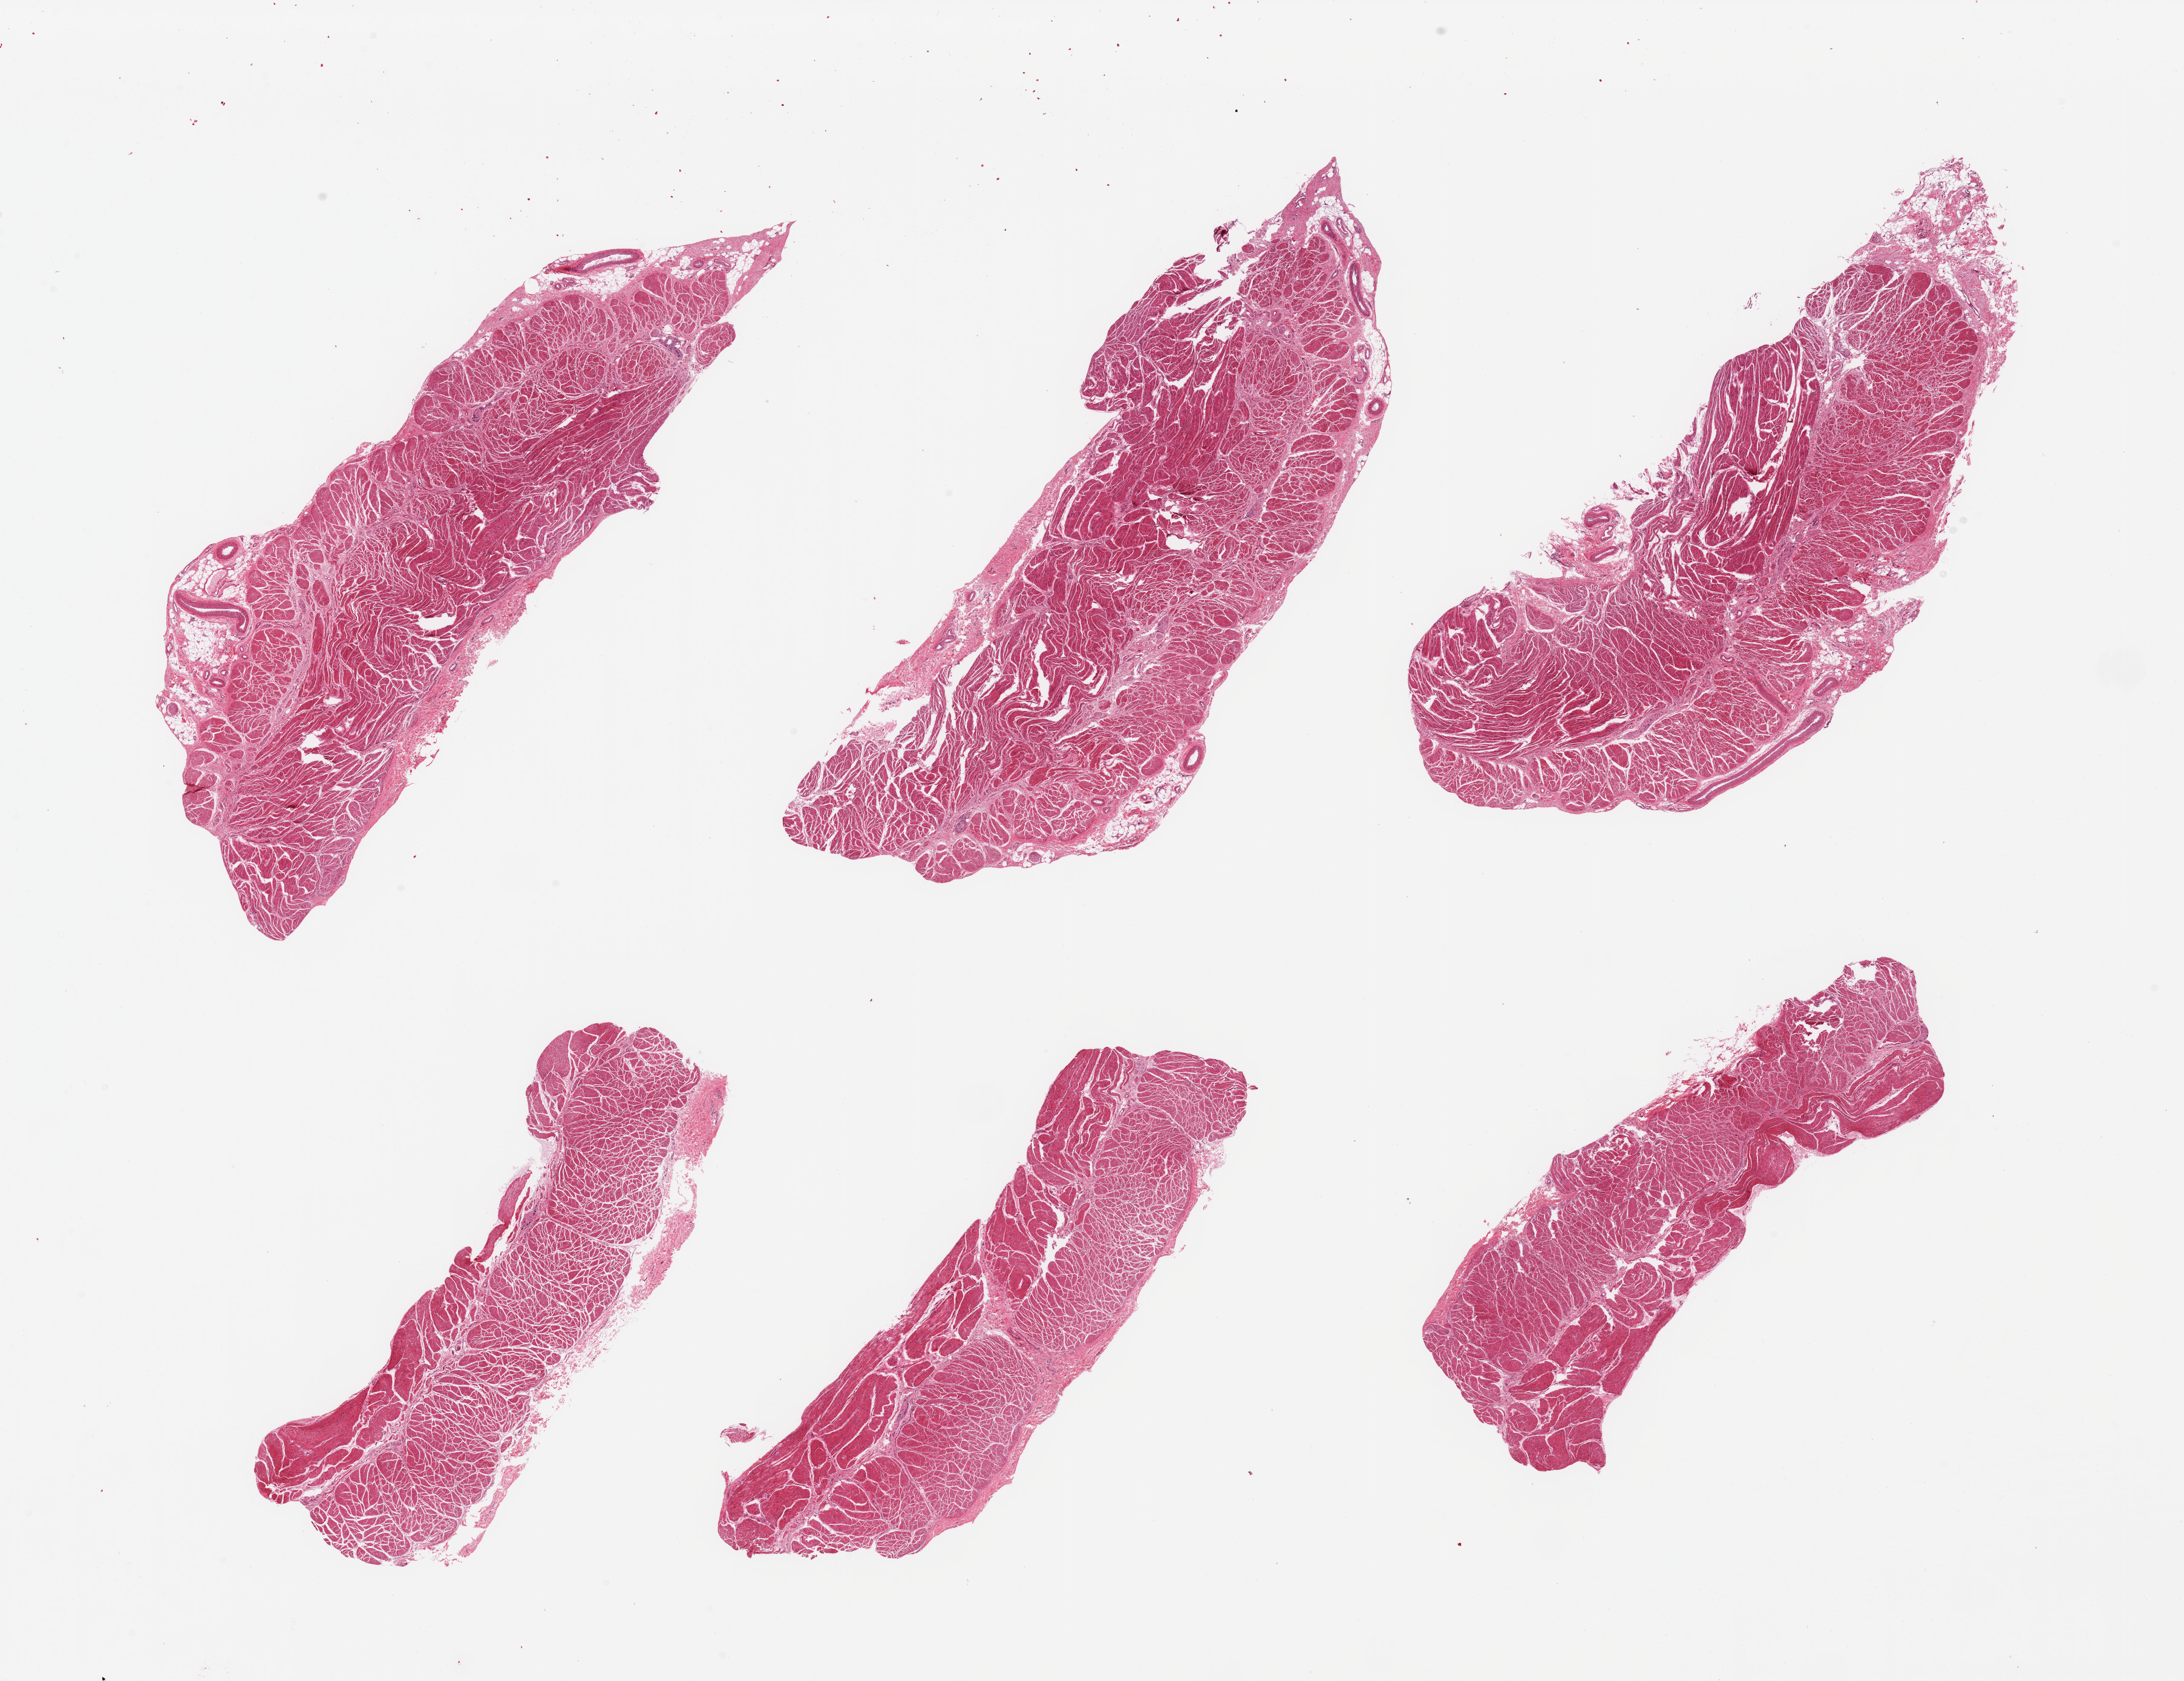
Whole-slide image, H&E stain, shown as a low-resolution overview of the whole scanned area (about 28.5 x 22.0 mm). PAXgene-fixed, paraffin-embedded tissue. Section of gastroesophageal junction (target tissue). Donor tissue sample.
Reviewer comment on this tissue sample: 6 pieces; well dissected muscularis propria.